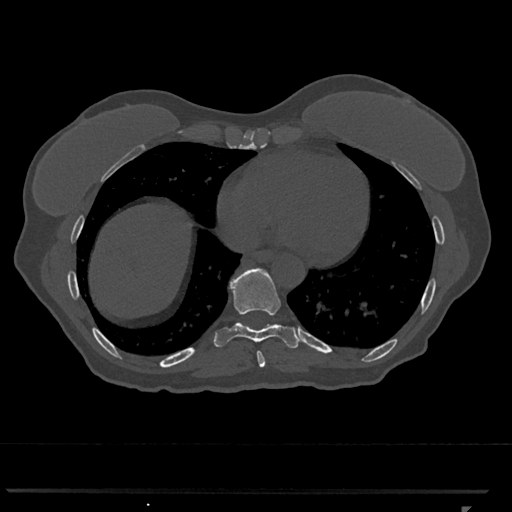
CT including the spine, one axial slice. Position 618 of 793 along the scan axis. Reconstruction kernel Br40s/3. 120 kVp. Bone window (W 1800 / L 400 HU). 0.5 mm slice thickness. 512 × 512 image matrix. Patient: female, 62 years. From the clinical record (not read from this slice): primary cancer: renal.
Structures marked on this image (semi-automatic segmentation, software-assisted and operator-edited):
- T8 vertebra: box from (x=257, y=351) to (x=266, y=367) px
- T9 vertebra: (x=214, y=268)–(x=299, y=349)